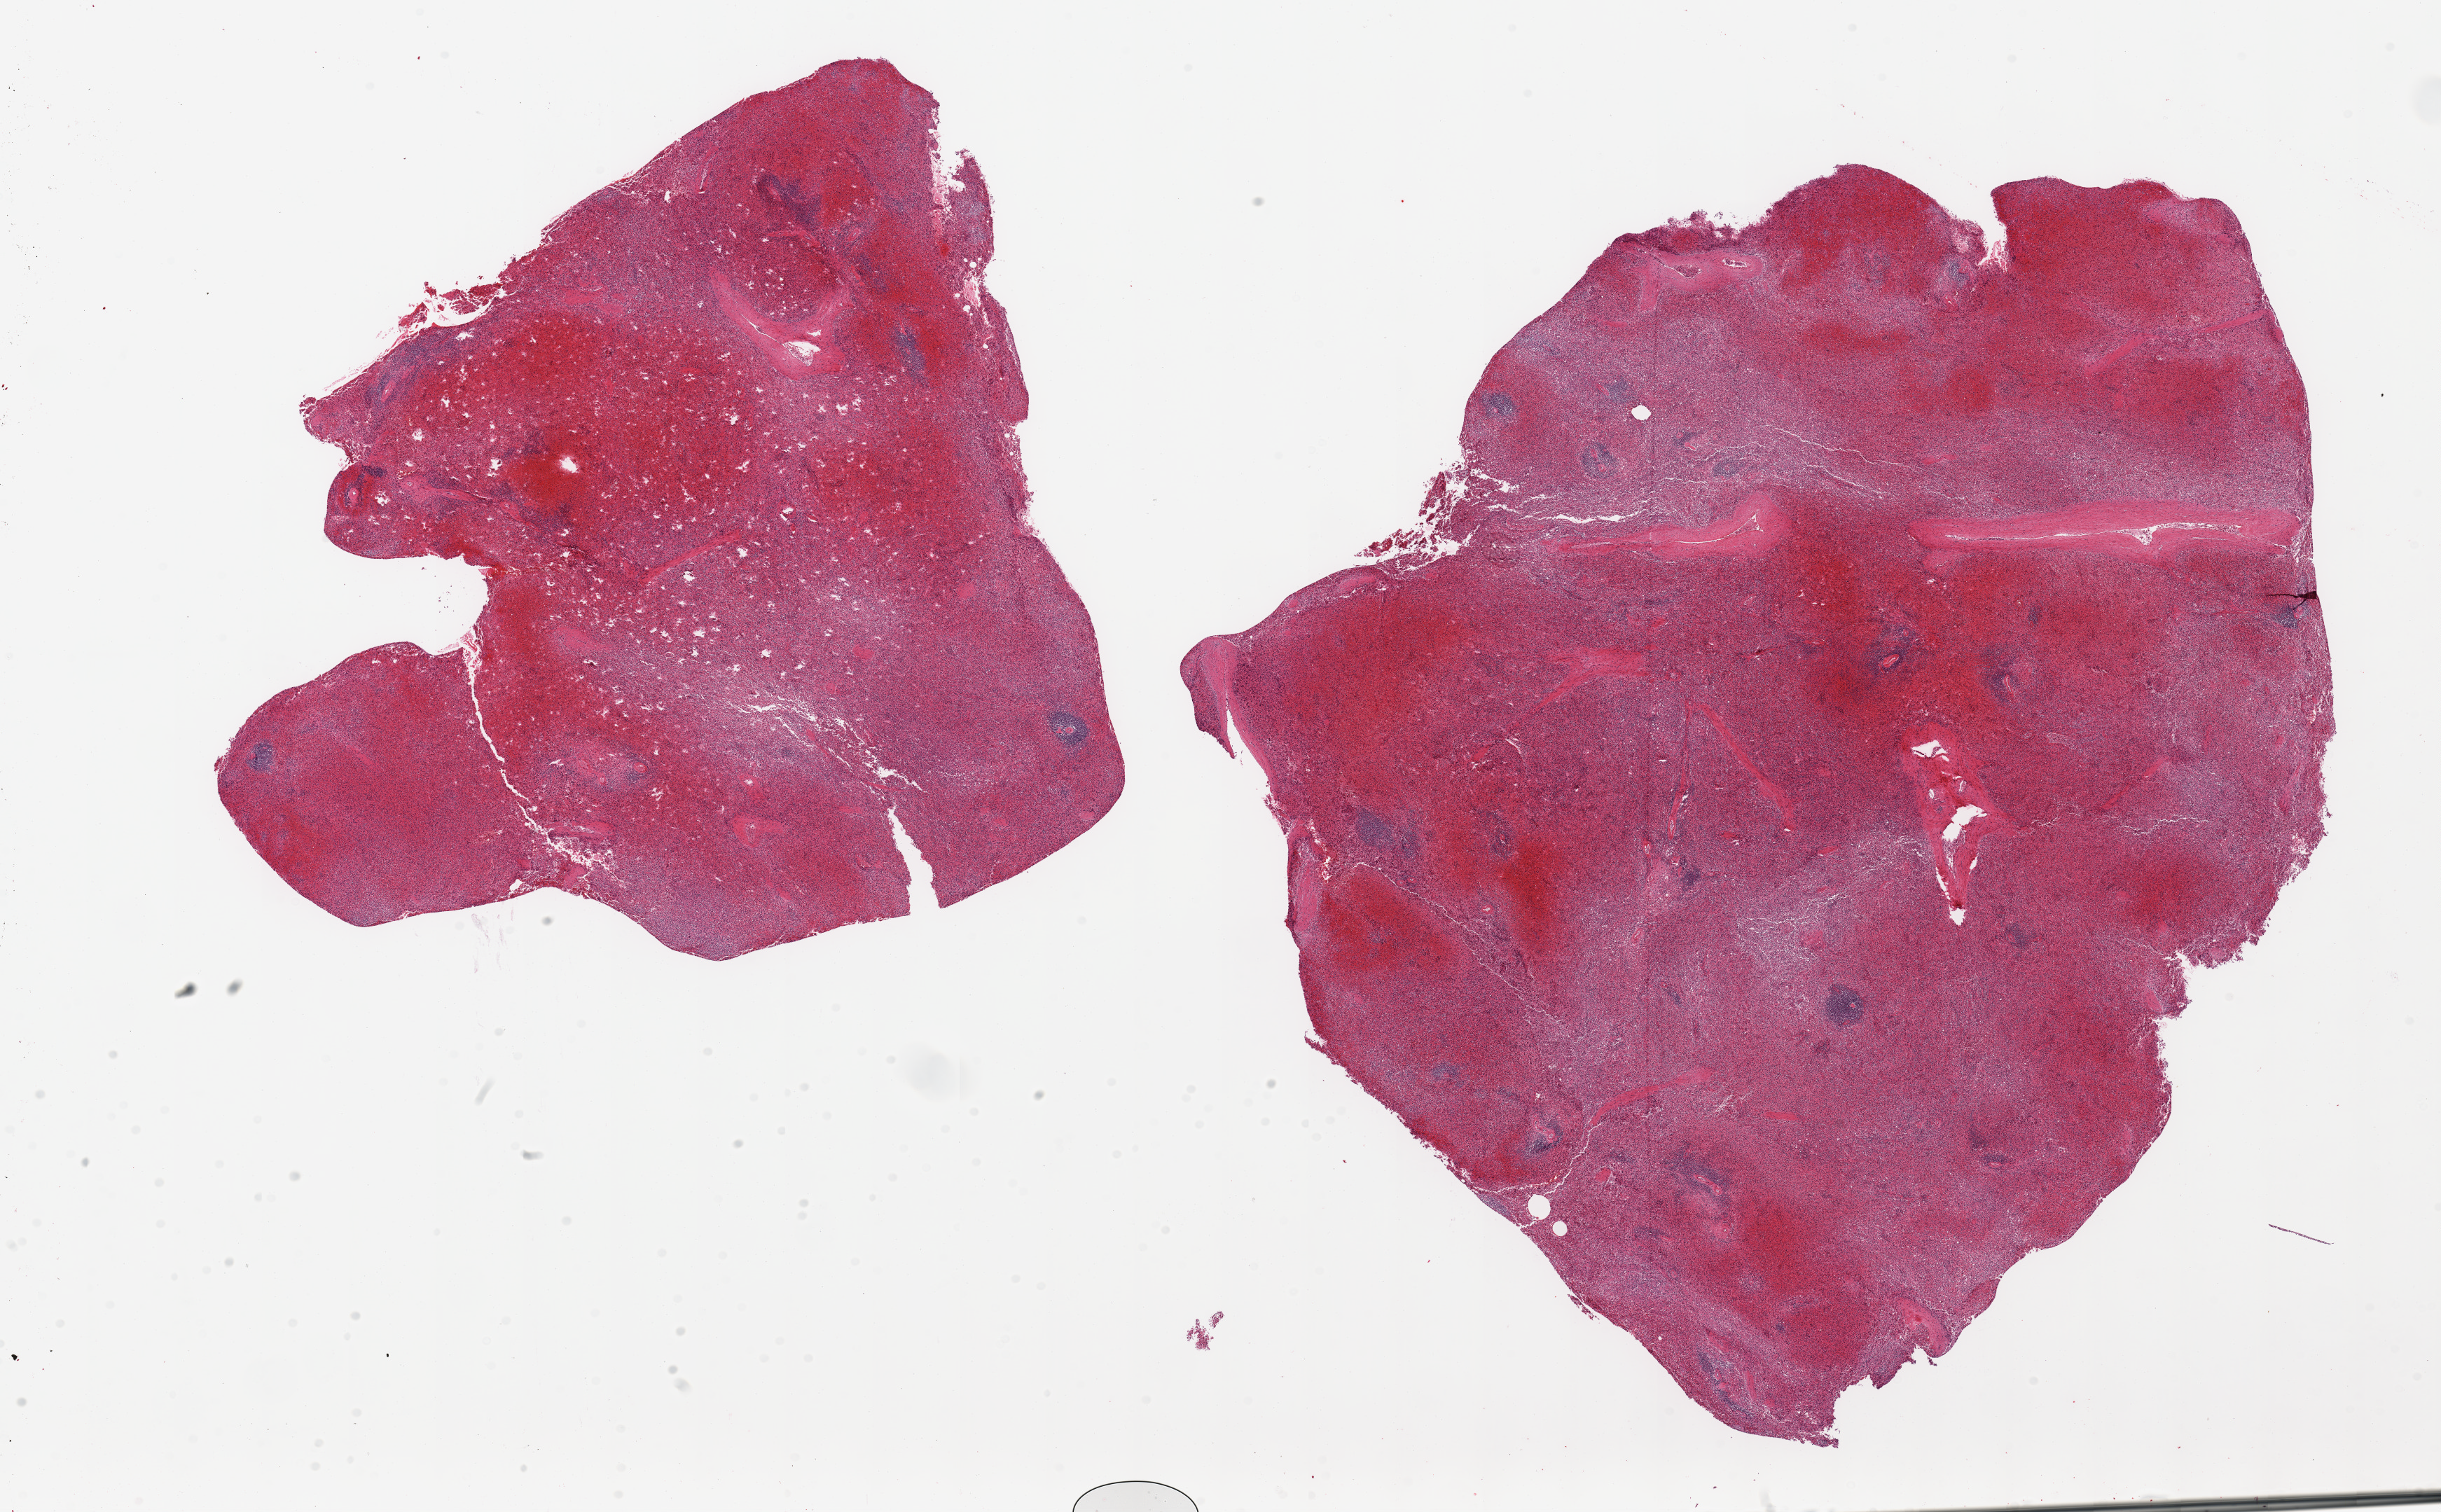
Digitized haematoxylin and eosin-stained section — shown as a low-resolution overview of the whole scanned area (about 27.6 x 17.1 mm); PAXgene-fixed paraffin-embedded (PFPE) section; target tissue: spleen; tissue donor sample.
- pathologist's review note for this sample: 2 pieces, marked congestion